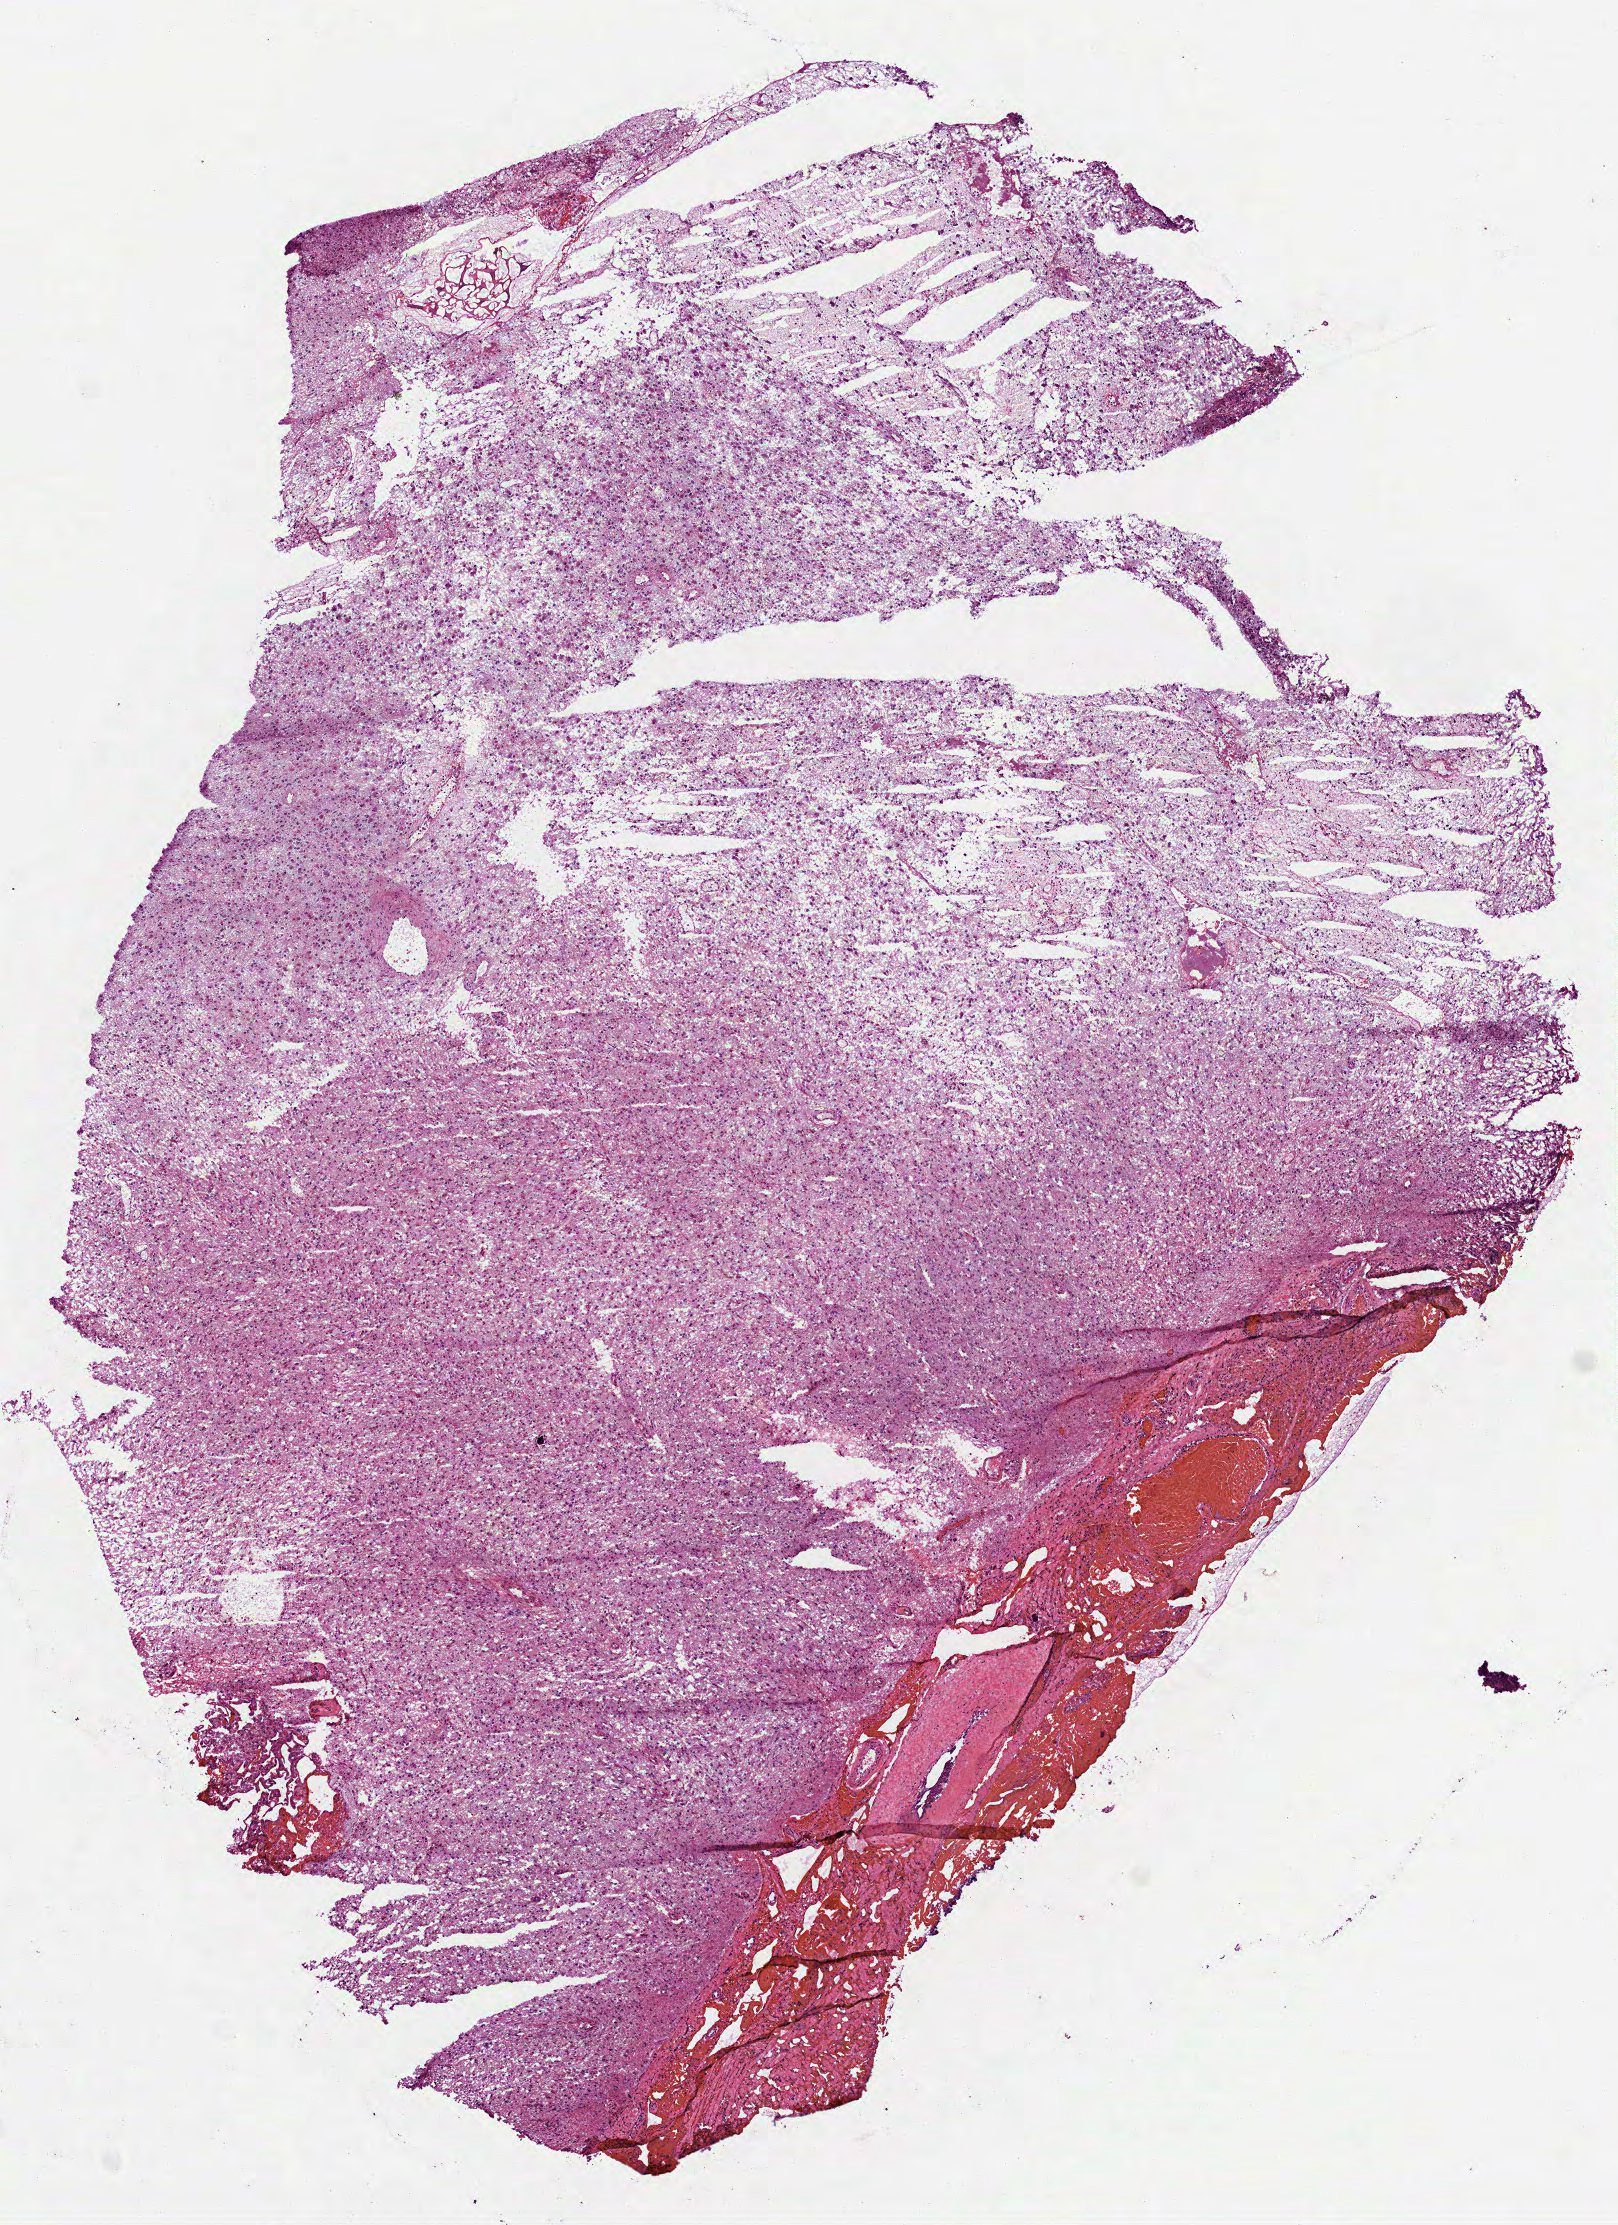
Whole-slide histology image, H&E, low-resolution overview of the scanned area, about 6.5 x 9.0 mm (slide scanned at 40x); frozen section; brain, primary tumour sample. Male, age 36 years at initial diagnosis. Histologic grade: G2 (moderately differentiated). Slide review estimates, as recorded: tumour cells 100%, tumour nuclei 75%, normal cells 0%, stromal cells 0%, necrosis 0%.
Pathologic diagnosis: Astrocytoma, NOS (cerebrum).